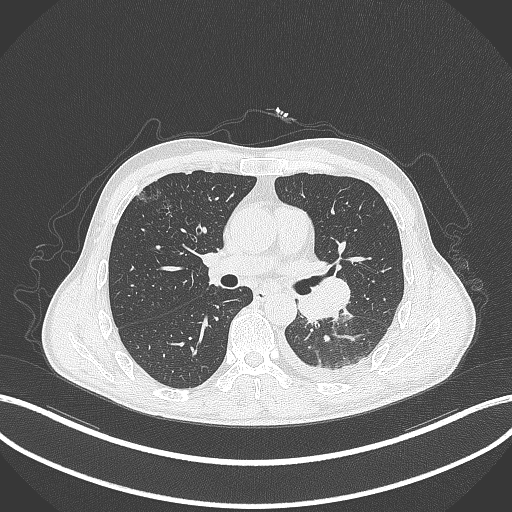
Chest CT, one axial slice. Reconstruction kernel B70f. Lung window (W 1500 / L -600 HU). 1 mm slice thickness. 512 × 512 image matrix, field of view 400 × 400 mm. Male patient, age 47 years. Case-level facts recorded for this patient, not image findings: clinical TNM (as recorded): T3 N1 M1c; histopathological grade: G3.
Annotated regions visible in this slice (rectangle marked by the reading radiologist):
- lung tumour (recorded histology: small cell carcinoma): box from (x=295, y=275) to (x=352, y=323) px